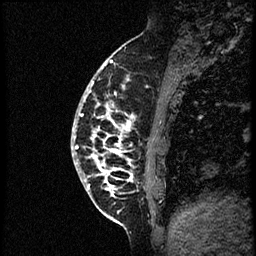
Breast MRI (dynamic contrast-enhanced), one sagittal slice; slice 17 of 56 in the series (ordered by position); dynamic contrast-enhanced study with each time point stored as its own series, time point 2 of 3 at this slice position (early post-contrast, ordered by acquisition time); 1.5 T; TE 4.2 ms, TR 21.3 ms; 256 × 256 image matrix, field of view 200 × 200 mm. Female patient, age 41 years. From the clinical record (not read from this slice): setting: breast cancer imaged before/during neoadjuvant chemotherapy; receptor status: HER2-positive.
Outlined on this slice (semi-automatic segmentation, software-assisted and operator-edited):
- analysis volume of interest (the breast-tissue region the enhancement analysis was run in; not a lesion): bounding box (x1, y1, x2, y2) in pixels: (71, 73, 177, 205)
- tumour enhancement mask (voxels above the 100 % enhancement threshold inside the analysis volume of interest): (74, 81, 133, 195)